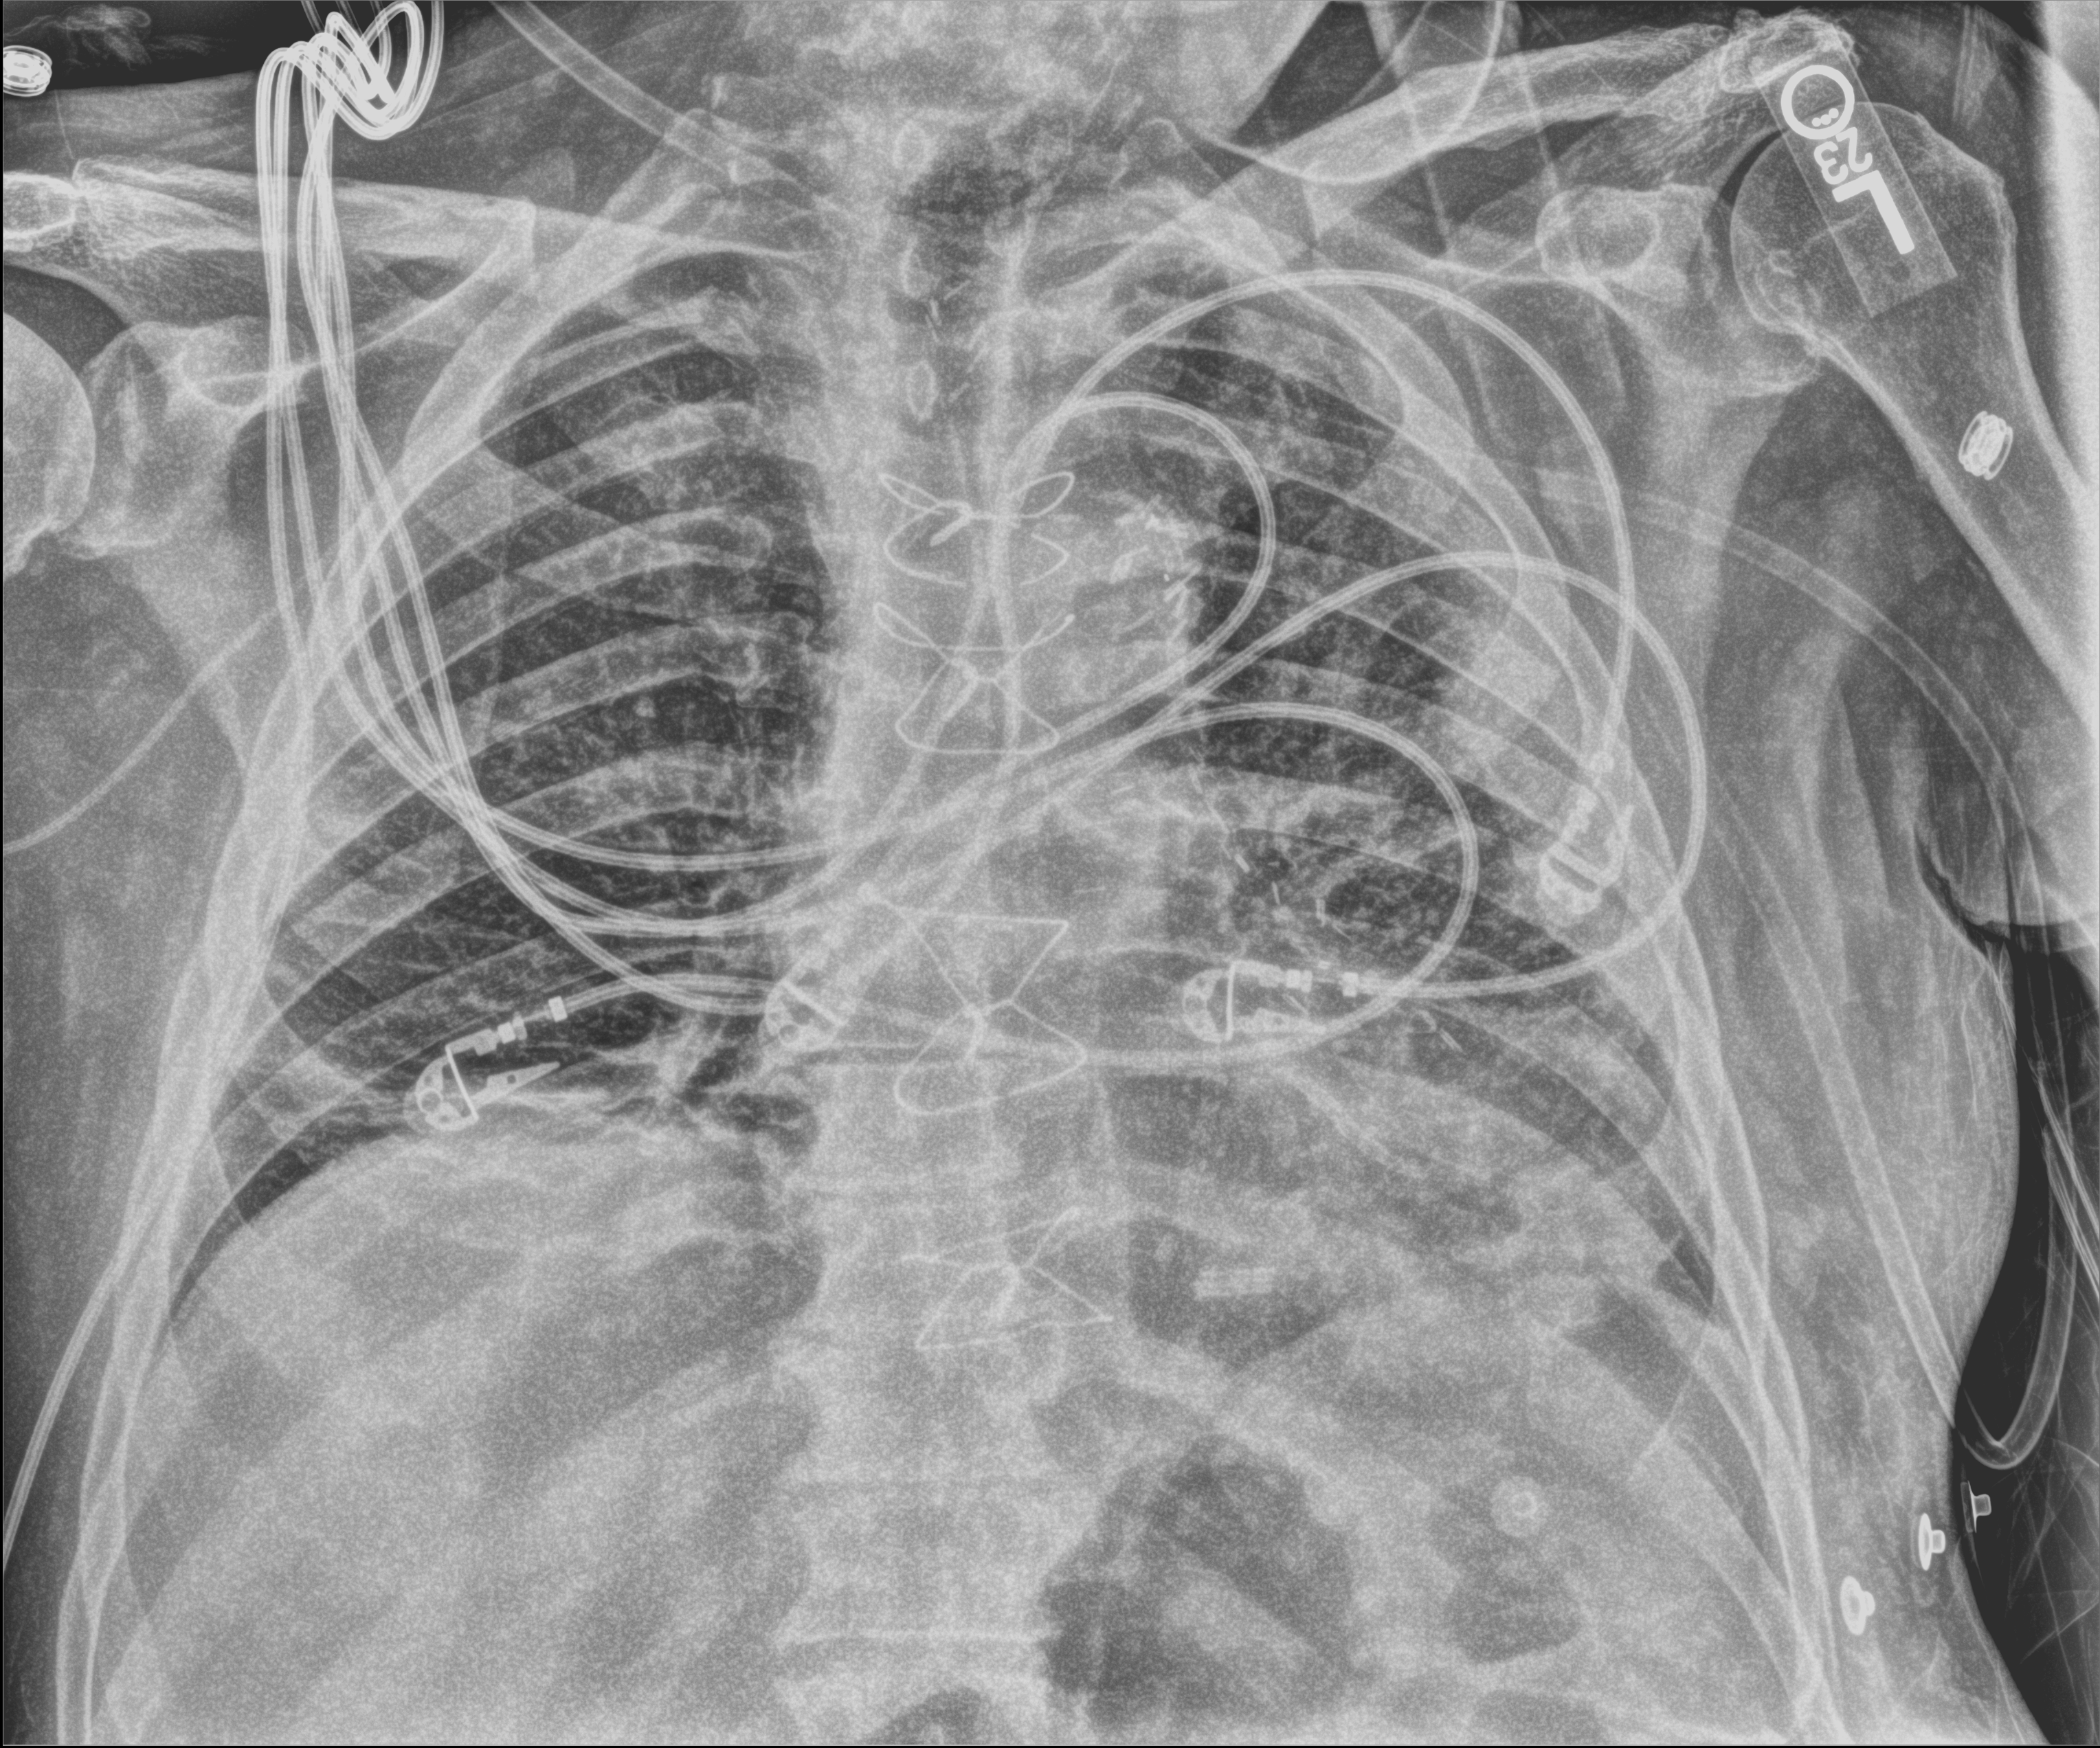
Chest X-ray (portable); anteroposterior (AP) projection. Patient hospitalised with COVID-19; male, aged 60–74 years.
Admission-level facts for this patient (not findings on this image; timing relative to this image not recorded): diabetes (admission record): yes; COPD (admission record): no; admitted to intensive care during this hospital stay: yes.